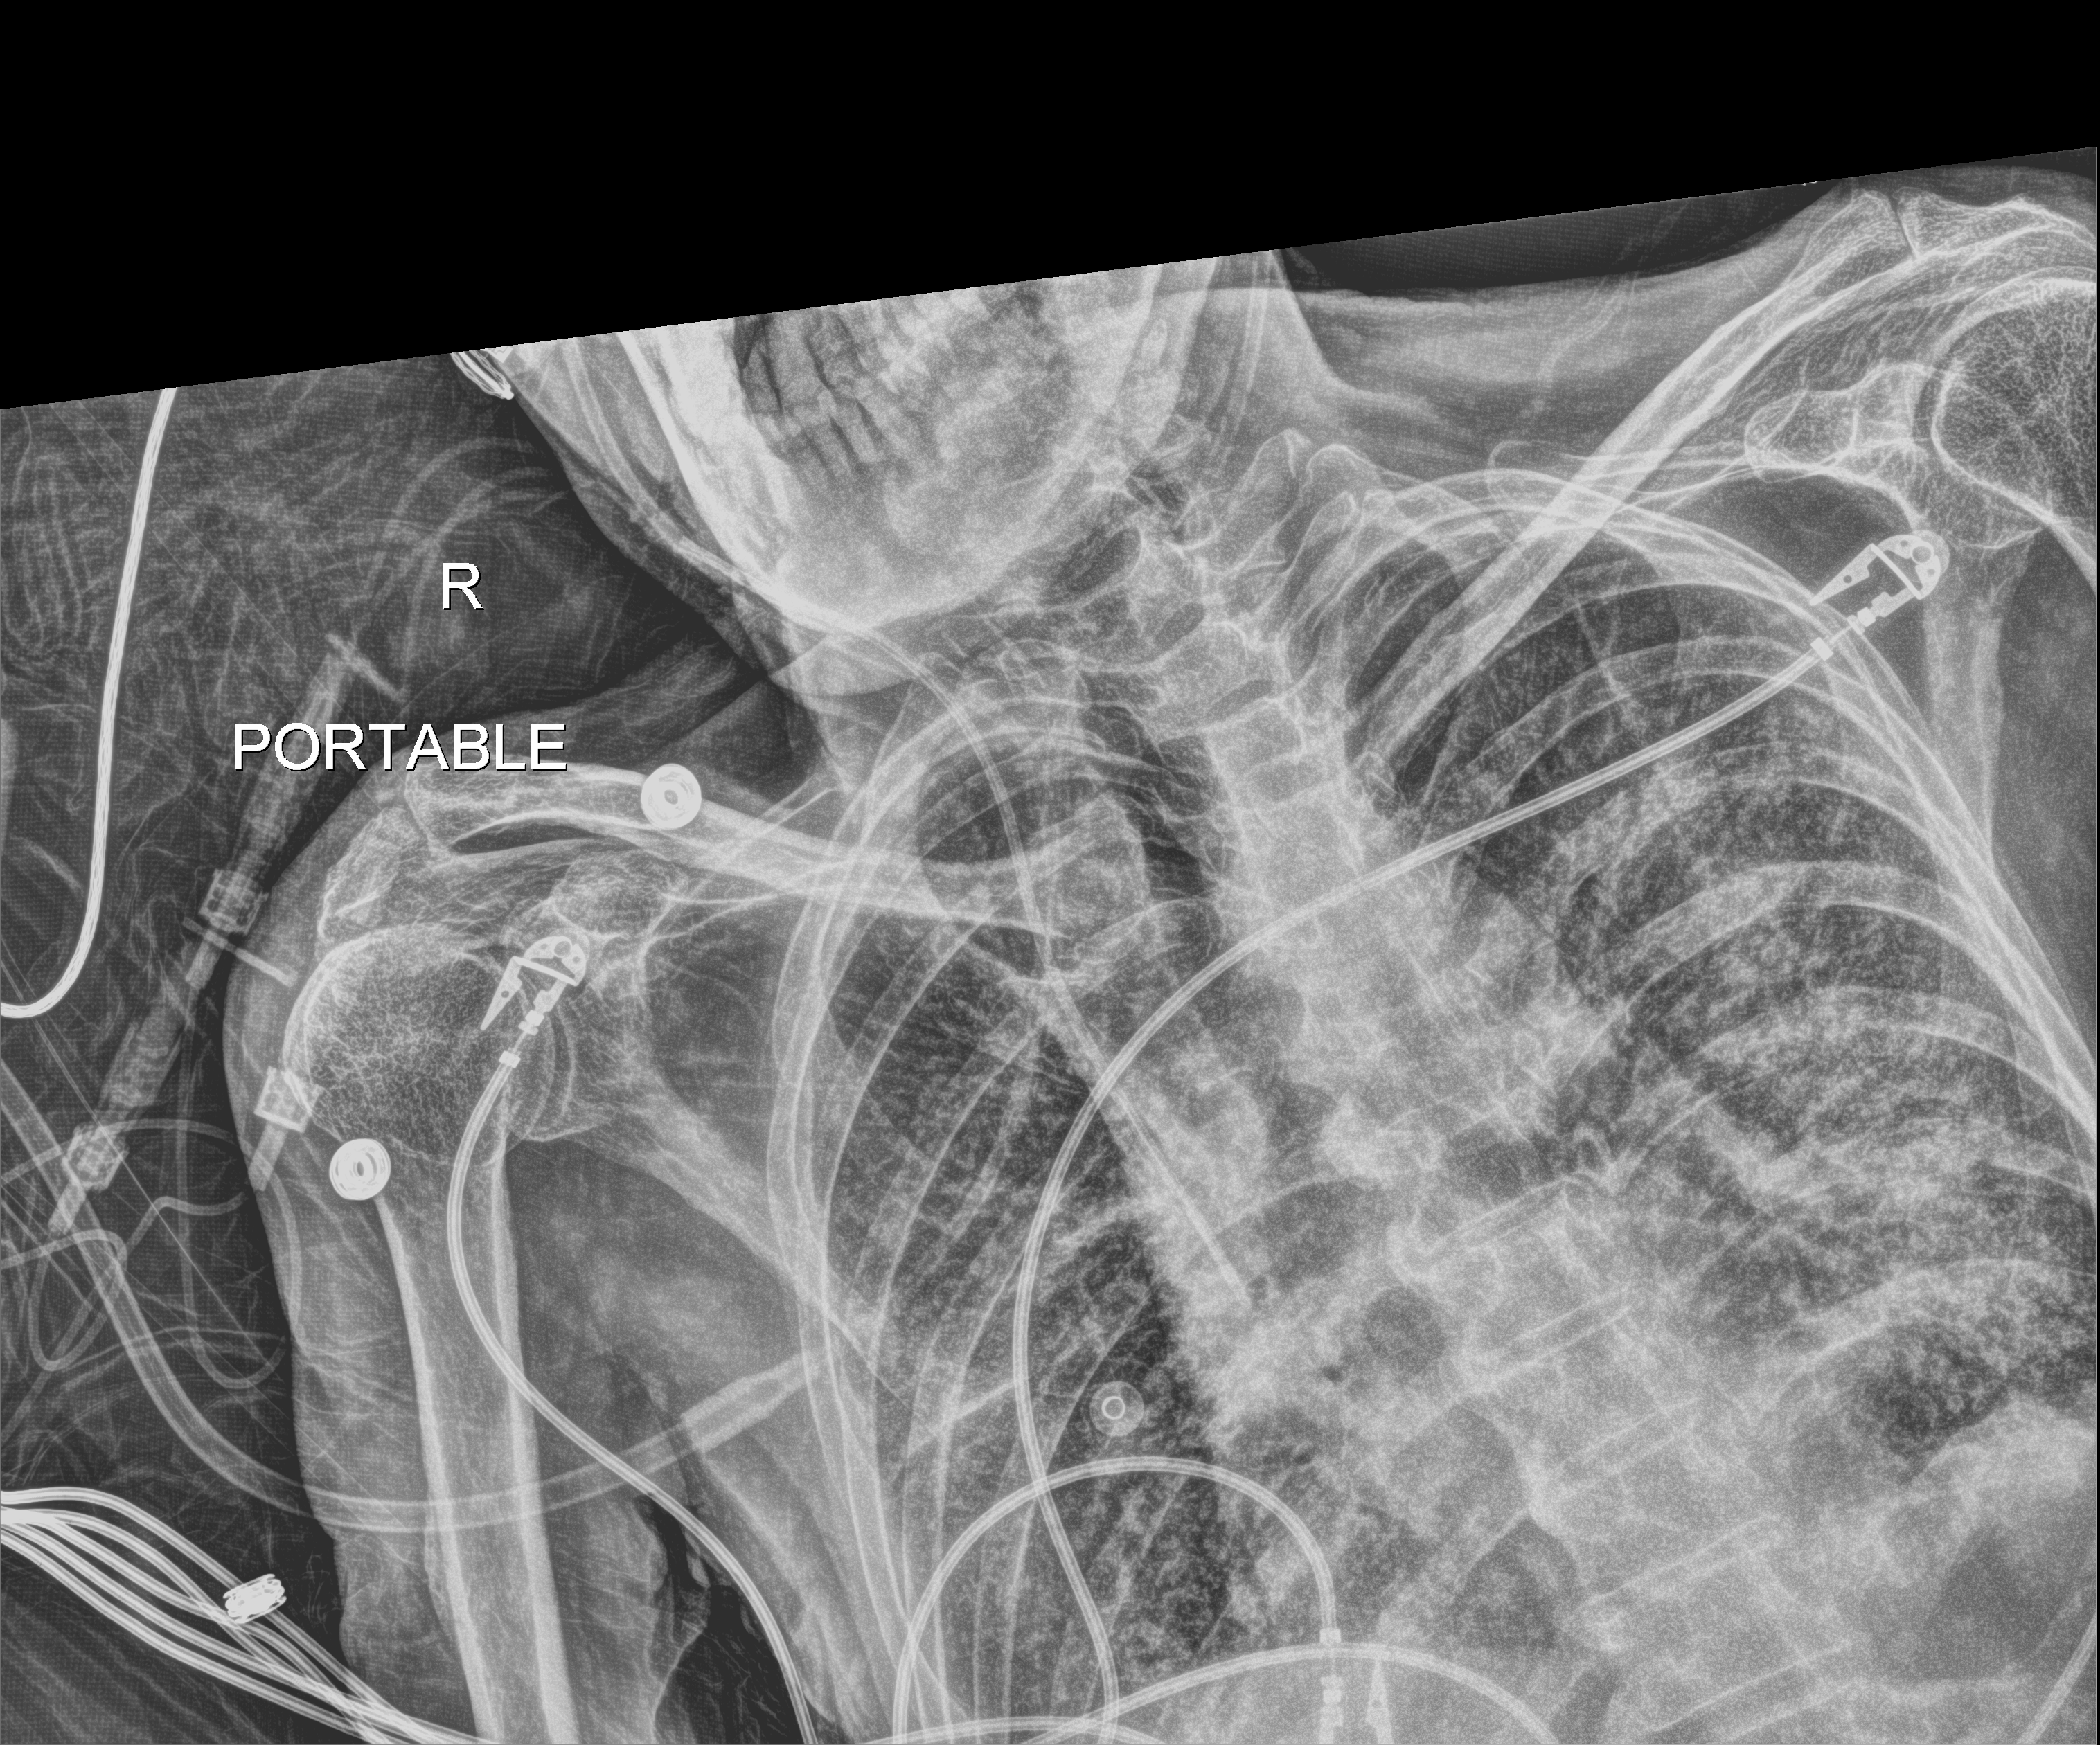
Bedside chest radiograph (digital radiography); anteroposterior (AP) projection. Male patient hospitalised with COVID-19, age 60–74 years.
Admission-level facts for this patient (not findings on this image; timing relative to this image not recorded):
- mechanically ventilated during this hospital stay: yes